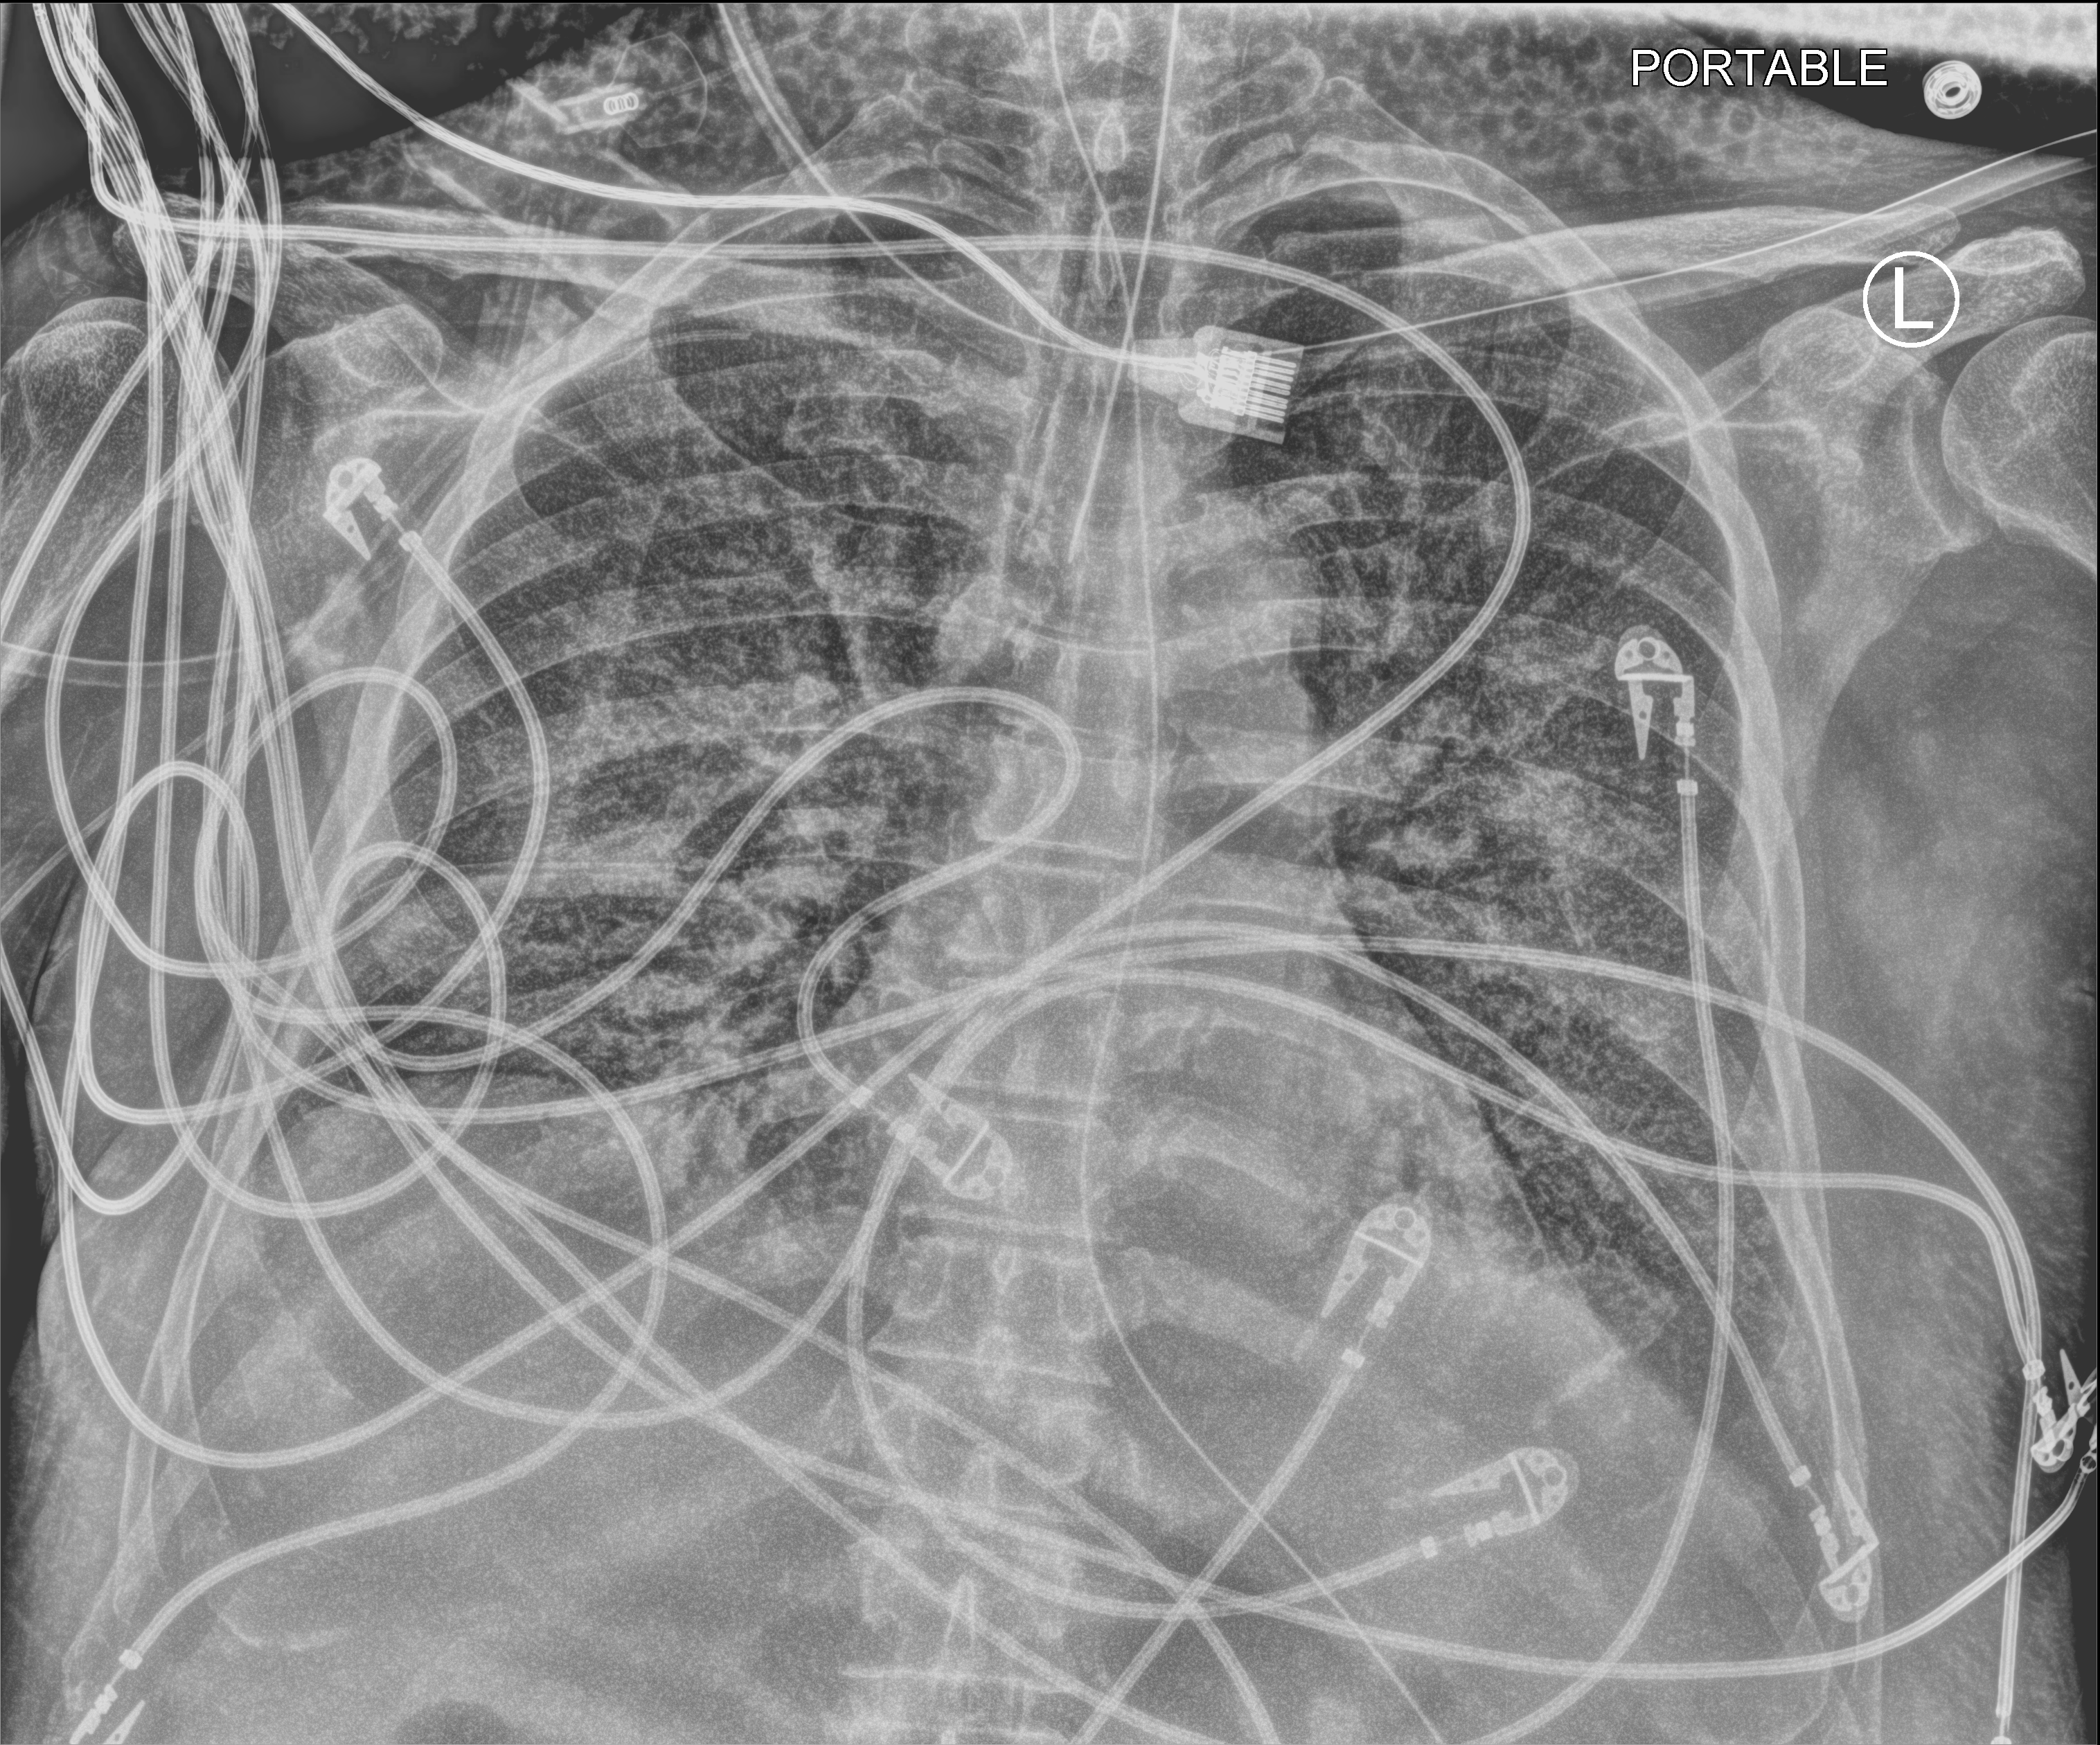
Portable chest radiograph; anteroposterior (AP) projection. Male patient hospitalised with COVID-19, age 60–74 years.
Admission-level facts for this patient (not findings on this image; timing relative to this image not recorded): smoking status (admission record): former; admitted to intensive care during this hospital stay: yes; other chronic lung disease (admission record): no.